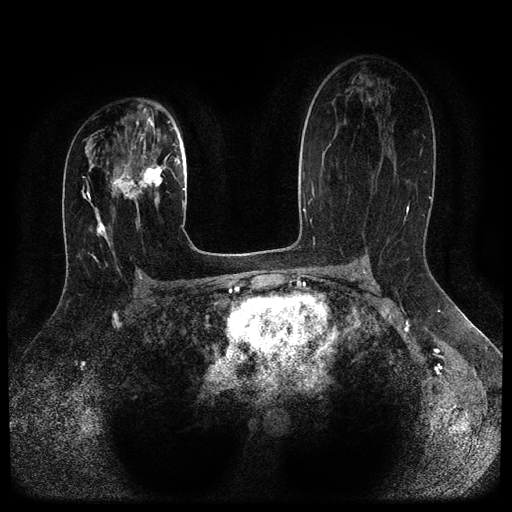
Breast MRI (dynamic contrast-enhanced, multi-phase), one axial slice; slice 62 of 116 in the series (ordered by position); dynamic contrast-enhanced series, time point 2 of 5 at this slice position (early post-contrast); 1.5 T; TE 2.6 ms, TR 5.4 ms; 512 × 512 image matrix, field of view 340 × 340 mm. Female patient, age 29 years.
Annotated regions visible in this slice (semi-automatically segmented with operator editing):
- breast lesion (labelled 'tumour' in the annotation; benign lesions carry a separate 'benign' label): bounding box [x1, y1, x2, y2] px = [106, 152, 170, 206]
- breast lesion (labelled benign in the annotation): [94, 207, 115, 255]